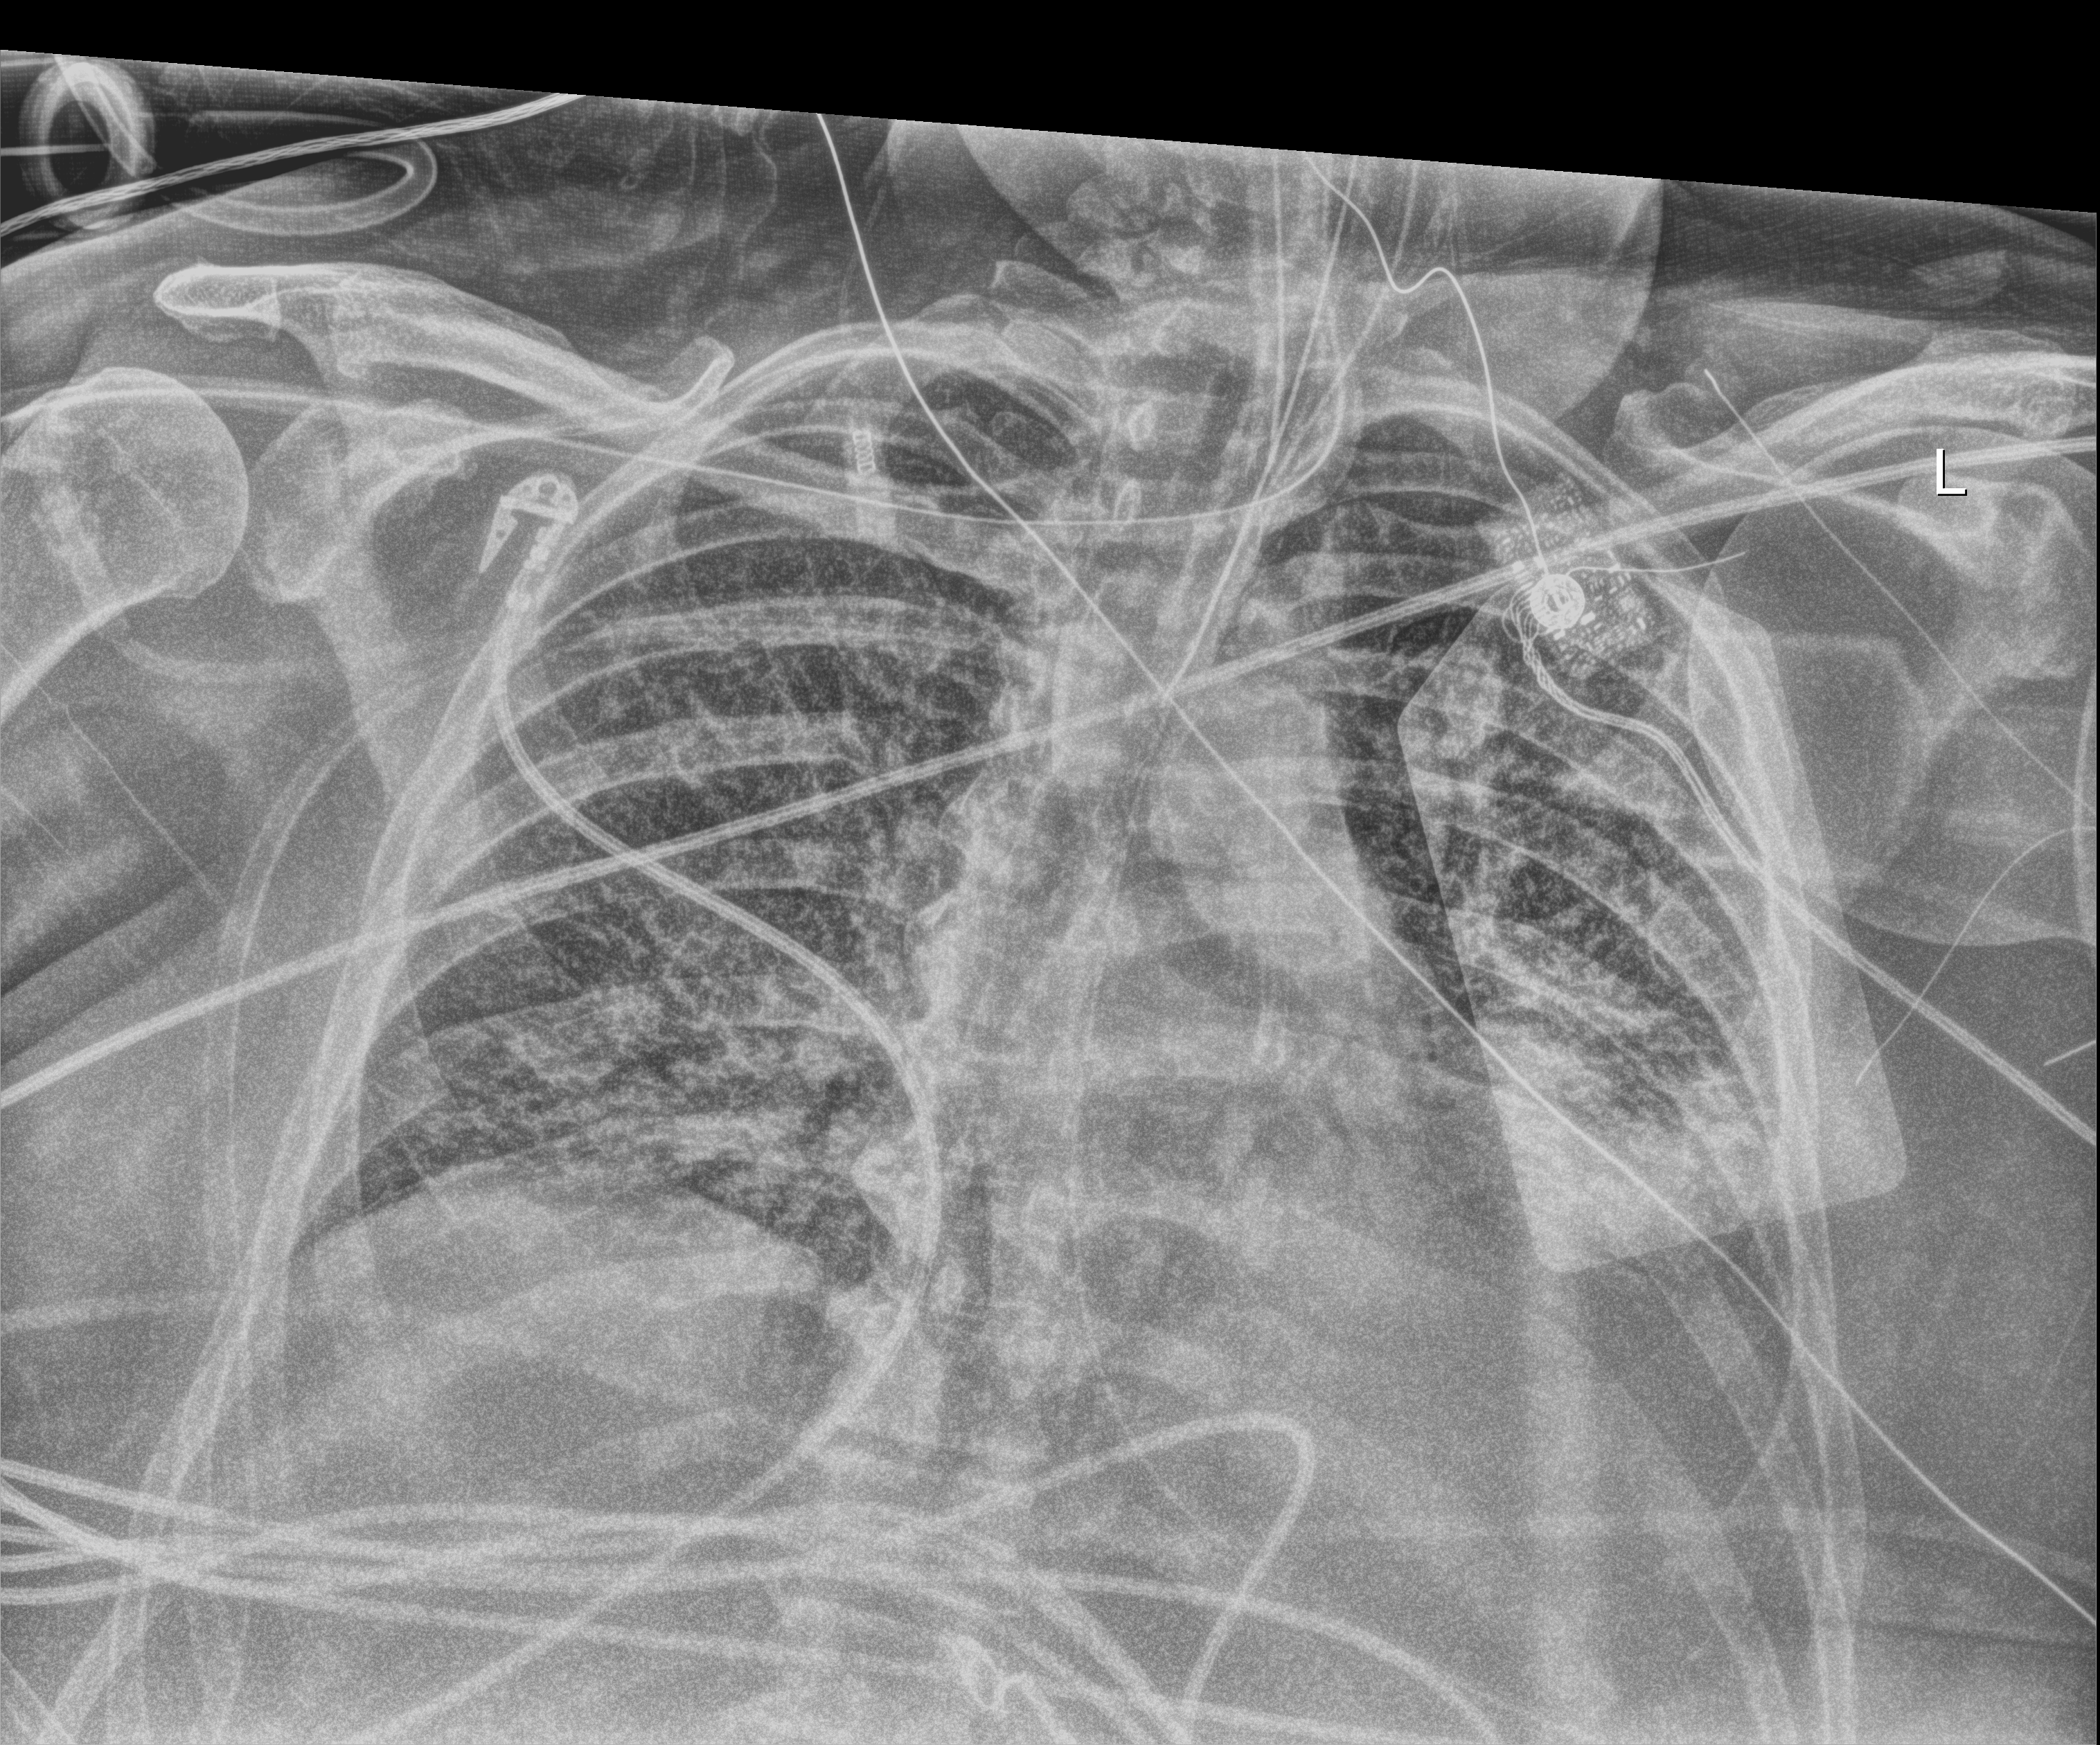
Chest X-ray (portable); anteroposterior (AP) projection. Patient hospitalised with COVID-19, aged 18–59 years.
Admission-level facts for this patient (not findings on this image; timing relative to this image not recorded):
- mechanically ventilated during this hospital stay: yes
- admitted to intensive care during this hospital stay: yes